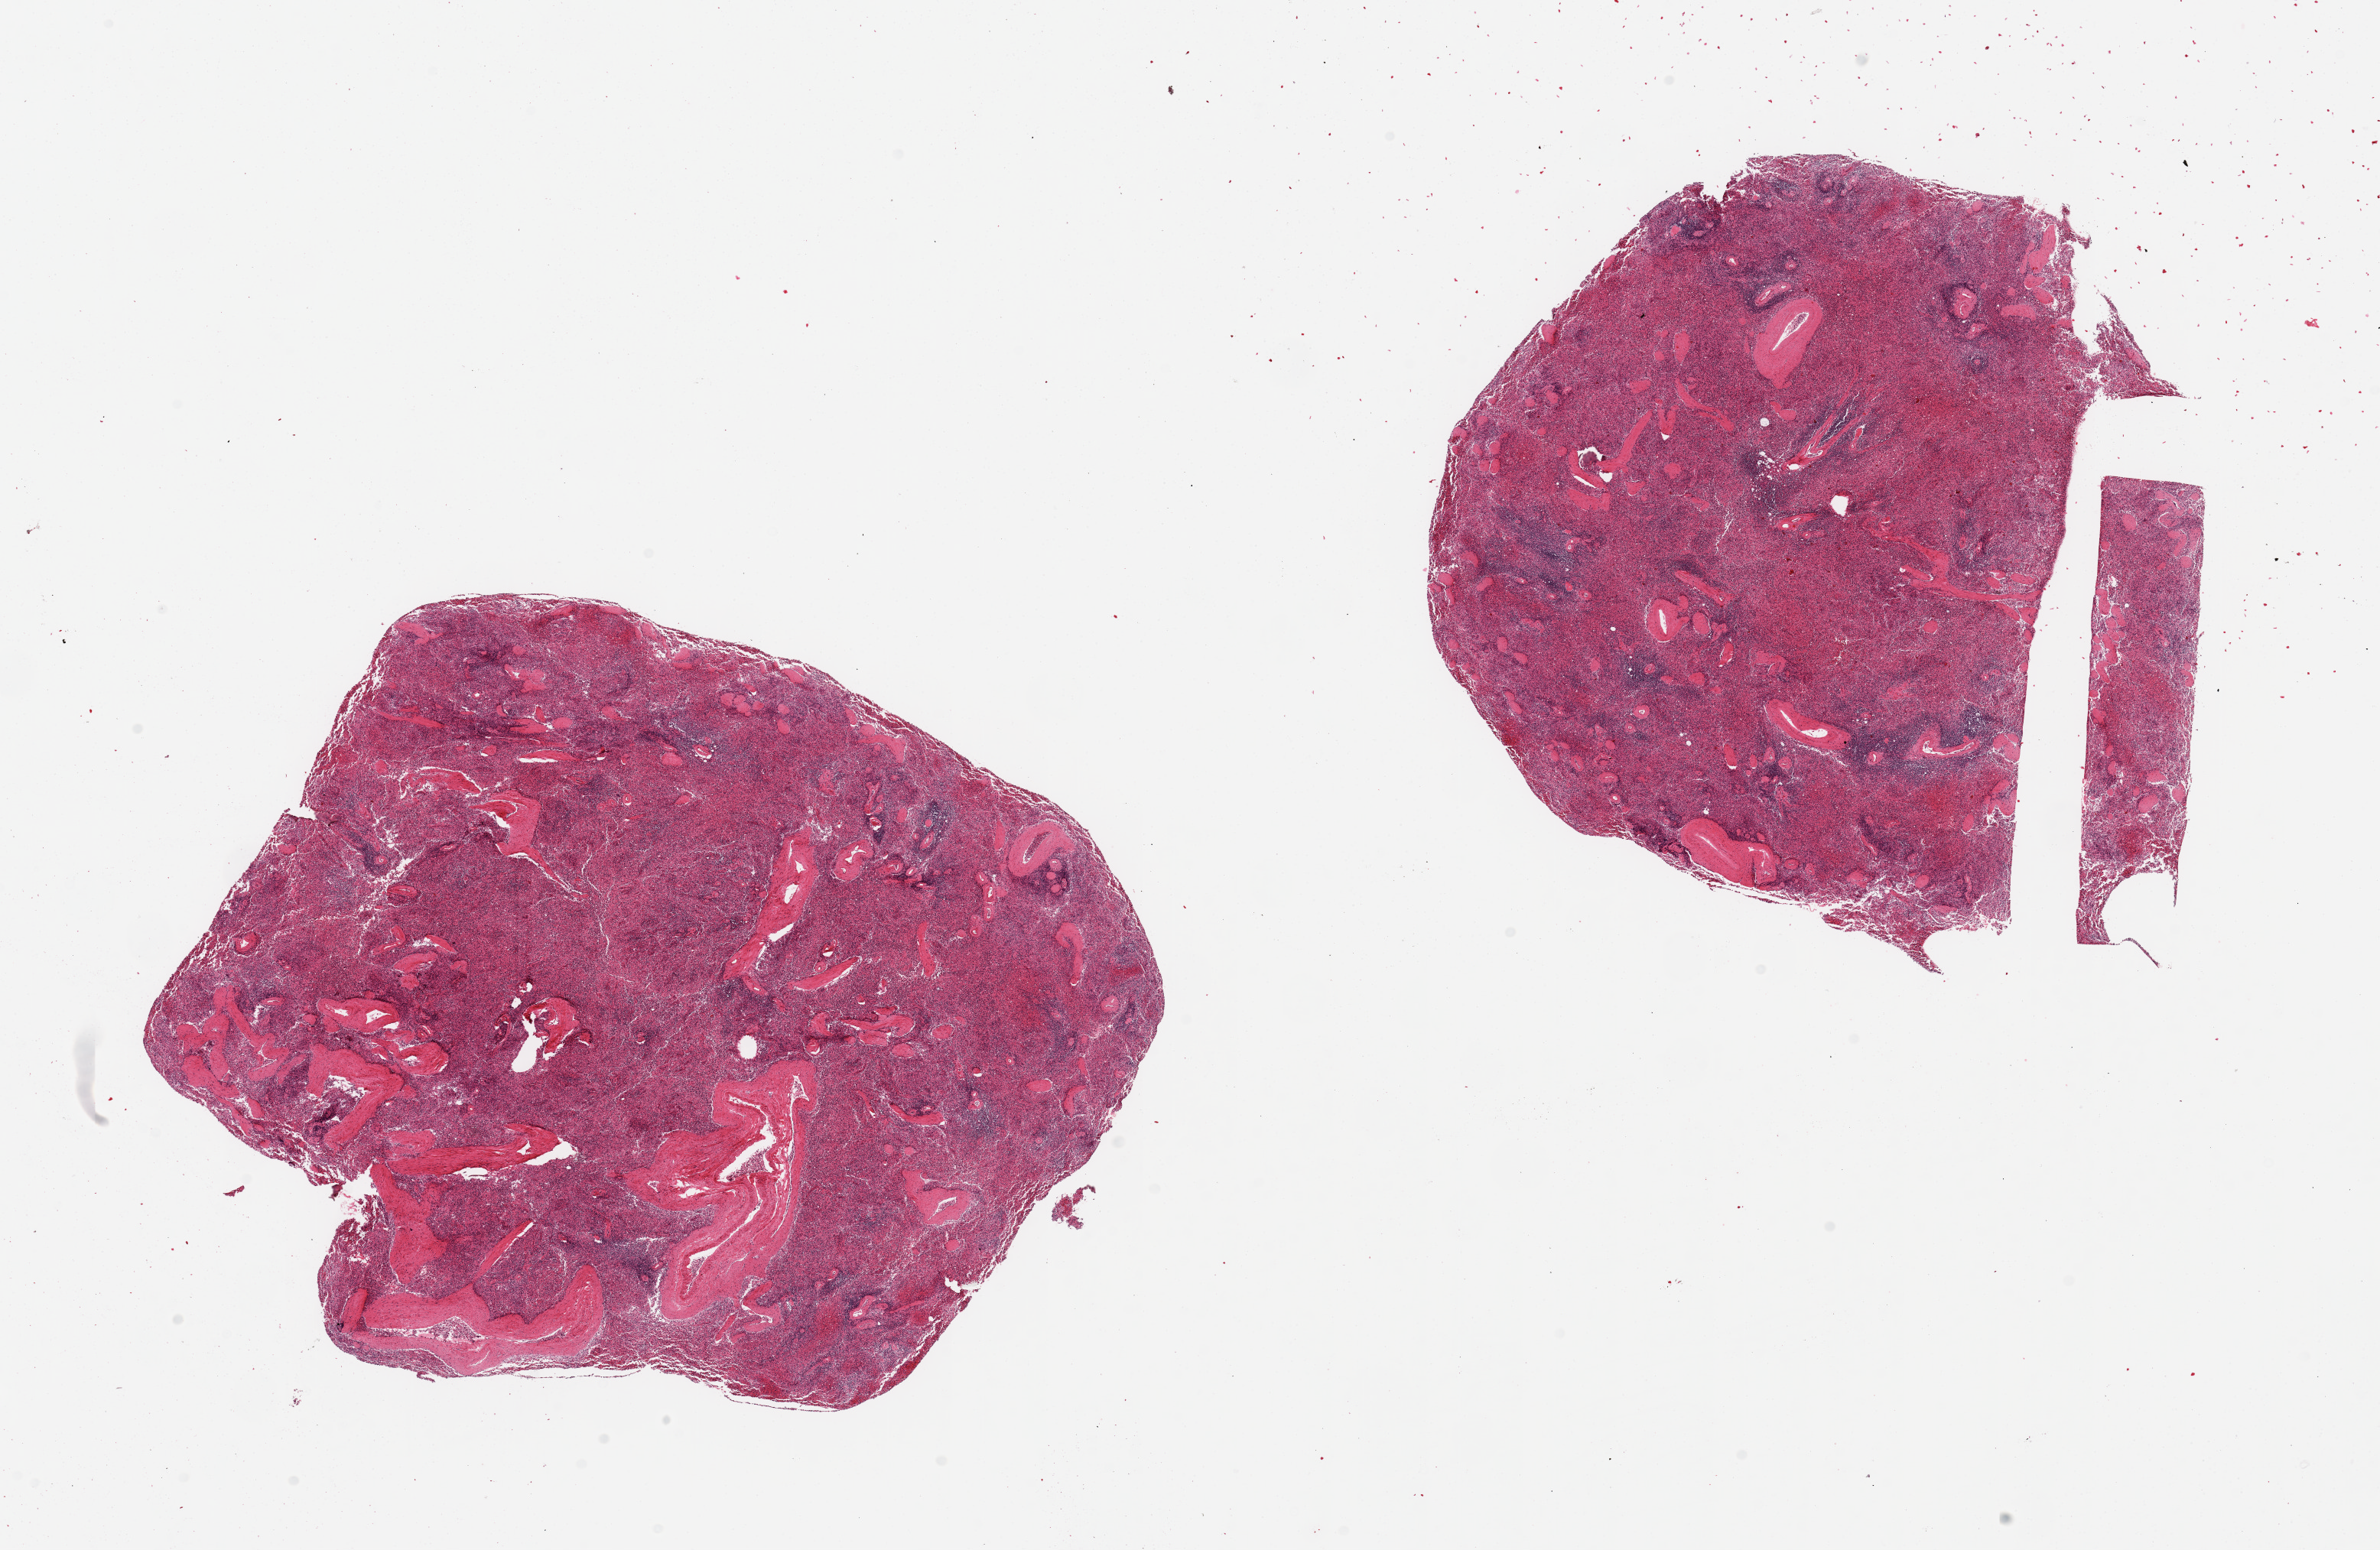
Digitized haematoxylin and eosin-stained section, a low-resolution overview of the entire scanned area, about 24.6 x 16.0 mm. PAXgene-fixed paraffin-embedded (PFPE) section. Sampled site (target tissue): spleen. Donor tissue sample. Donor: female.
Reviewer comment on this tissue sample: 2 pieces.